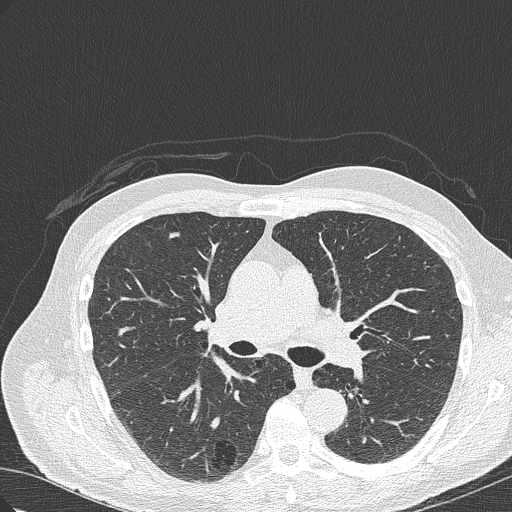
Chest CT (low-dose screening protocol), one axial image. Baseline screening round. Lung window (W 1500 / L -600 HU). Lung (sharp) reconstruction kernel (B50f). Slice 129 of 322 in the series. Male participant, aged 70 years at enrolment. Current smoker at enrolment.
Expert-annotated lung lesion, bounding box <199,419,263,473> (left, top, right, bottom; pixels). The screening reader recorded 4 non-calcified nodules or masses ≥4 mm on this exam (right lower lobe, right lower lobe, right upper lobe, right lower lobe); which of them this box marks is not recorded. Official screen result: positive, change unspecified: nodule(s) >= 4 mm or enlarging nodule(s), mass(es), or other non-specific abnormalities suspicious for lung cancer. Later outcome: lung cancer diagnosed 978 days after this screen — bronchiolo-alveolar adenocarcinoma, NOS, right lower lobe, poorly differentiated (G3), stage IB (AJCC 6th edition), 30 mm at pathology.